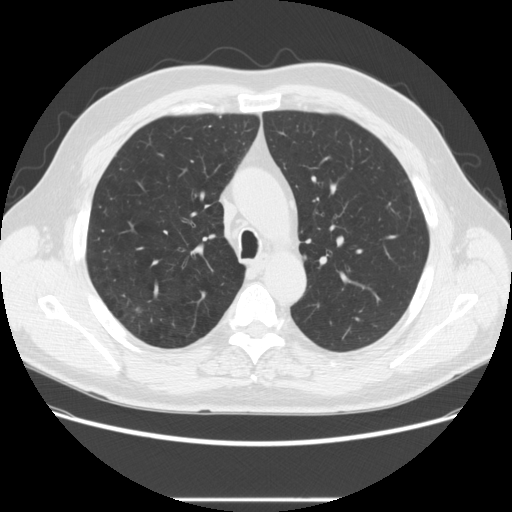
Chest CT (low-dose screening protocol), one axial image; baseline annual screen; lung window (W 1500 / L -600 HU); standard (soft-tissue) reconstruction kernel (STANDARD); slice 81 of 270 in the series. Male participant, aged 64 years at enrolment. Former smoker at enrolment.
- Expert reader's lesion annotation, bounding box (x1, y1, x2, y2) in pixels: (114, 298, 151, 326).
- The screening reader recorded 2 non-calcified nodules or masses ≥4 mm on this exam (right upper lobe, right upper lobe); which of them this box marks is not recorded.
- Participant outcome: lung cancer diagnosed 753 days after this screen — adenocarcinoma, NOS, right upper lobe, moderately differentiated (G2), stage IA (AJCC 6th edition), 14 mm at pathology.